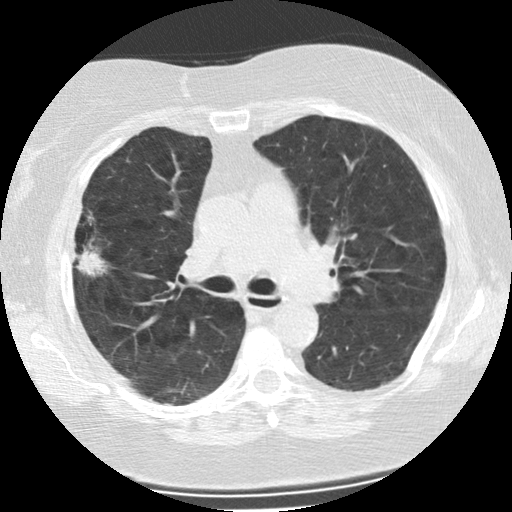
Low-dose screening chest CT, axial slice; second screening round (one year after baseline); lung window (W 1500 / L -600 HU); standard (soft-tissue) reconstruction kernel (STANDARD); slice 83 of 225 in the series. Female, age 73 years at enrolment. Former smoker at enrolment.
- Expert reader's lesion annotation, box from (x=55, y=214) to (x=111, y=285) px.
- The screening reader recorded 2 non-calcified nodules or masses ≥4 mm on this exam; which of them this box marks is not recorded.
- Lung cancer was diagnosed 47 days after this screen: bronchiolo-alveolar adenocarcinoma, NOS, right upper lobe, moderately differentiated (G2), stage IIIB (AJCC 6th edition), 21 mm at pathology.